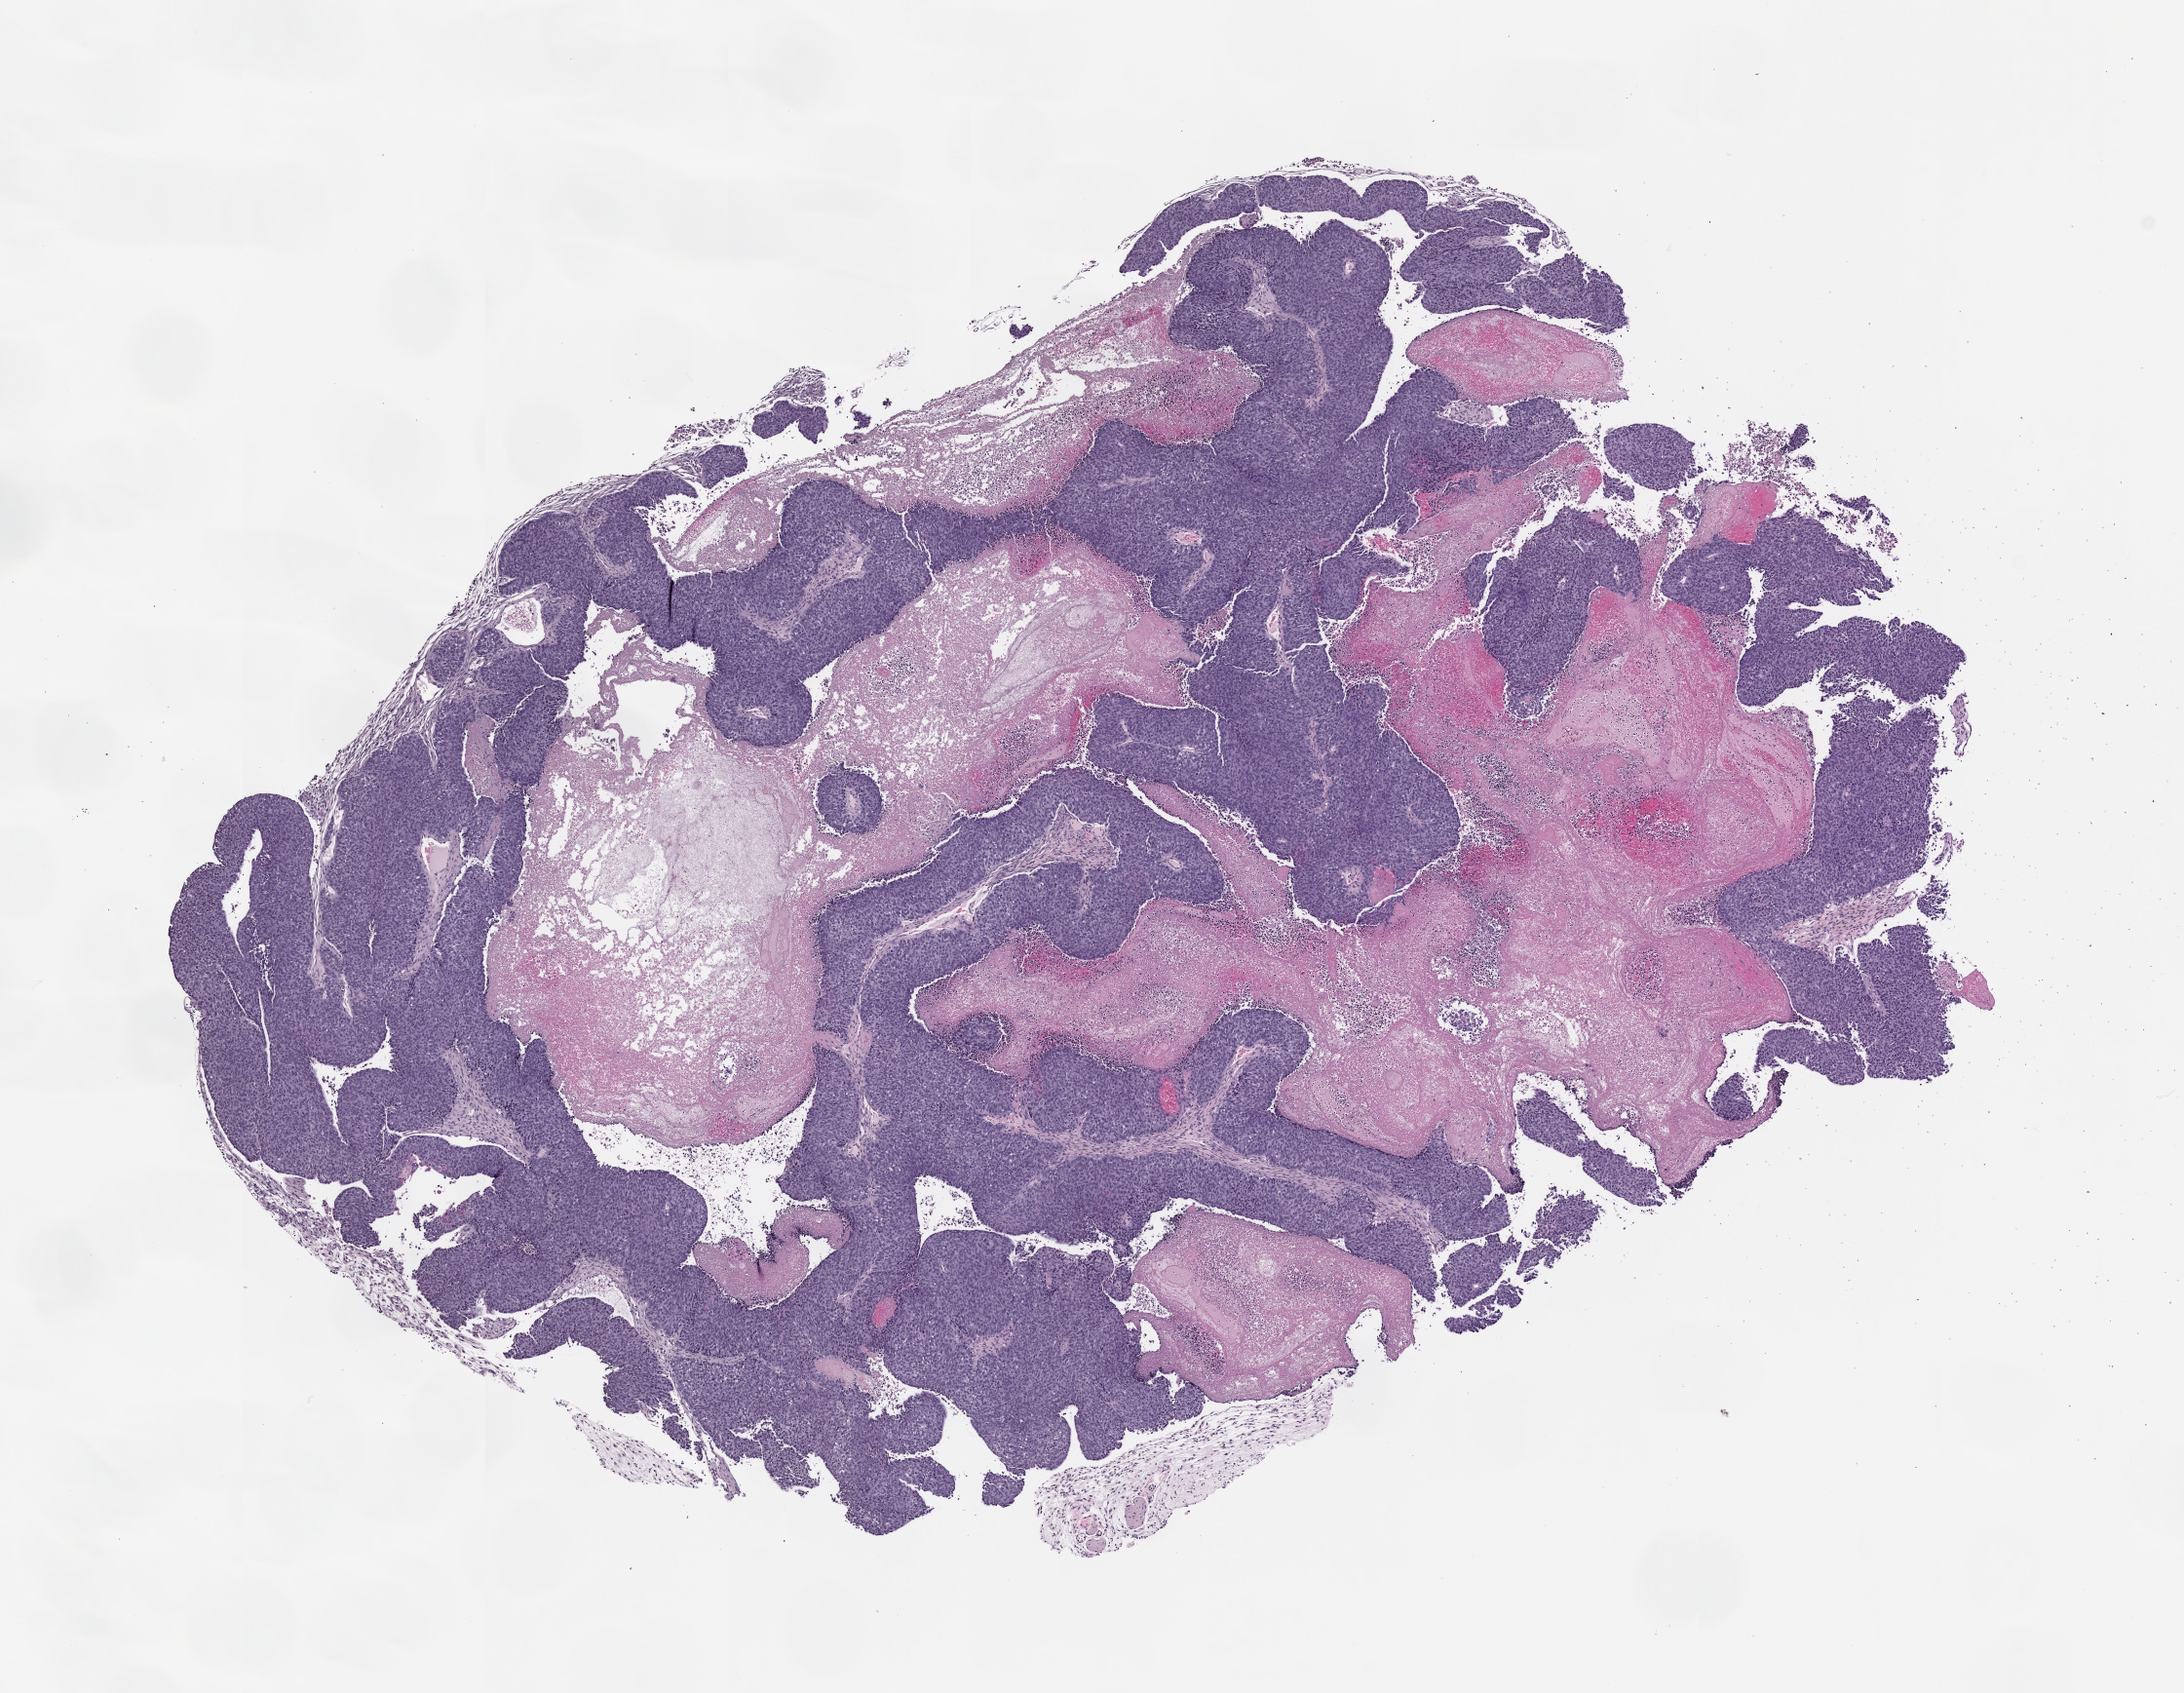
Hematoxylin and eosin (H&E) whole-slide image of a patient-derived xenograft (PDX) tumor grown in a mouse, passage 1 — shown as a low-resolution overview of the whole scanned area (about 9.0 x 7.0 mm), FFPE section, tumor site category: vagina.
Originating patient diagnosis: Vaginal Carcinoma.